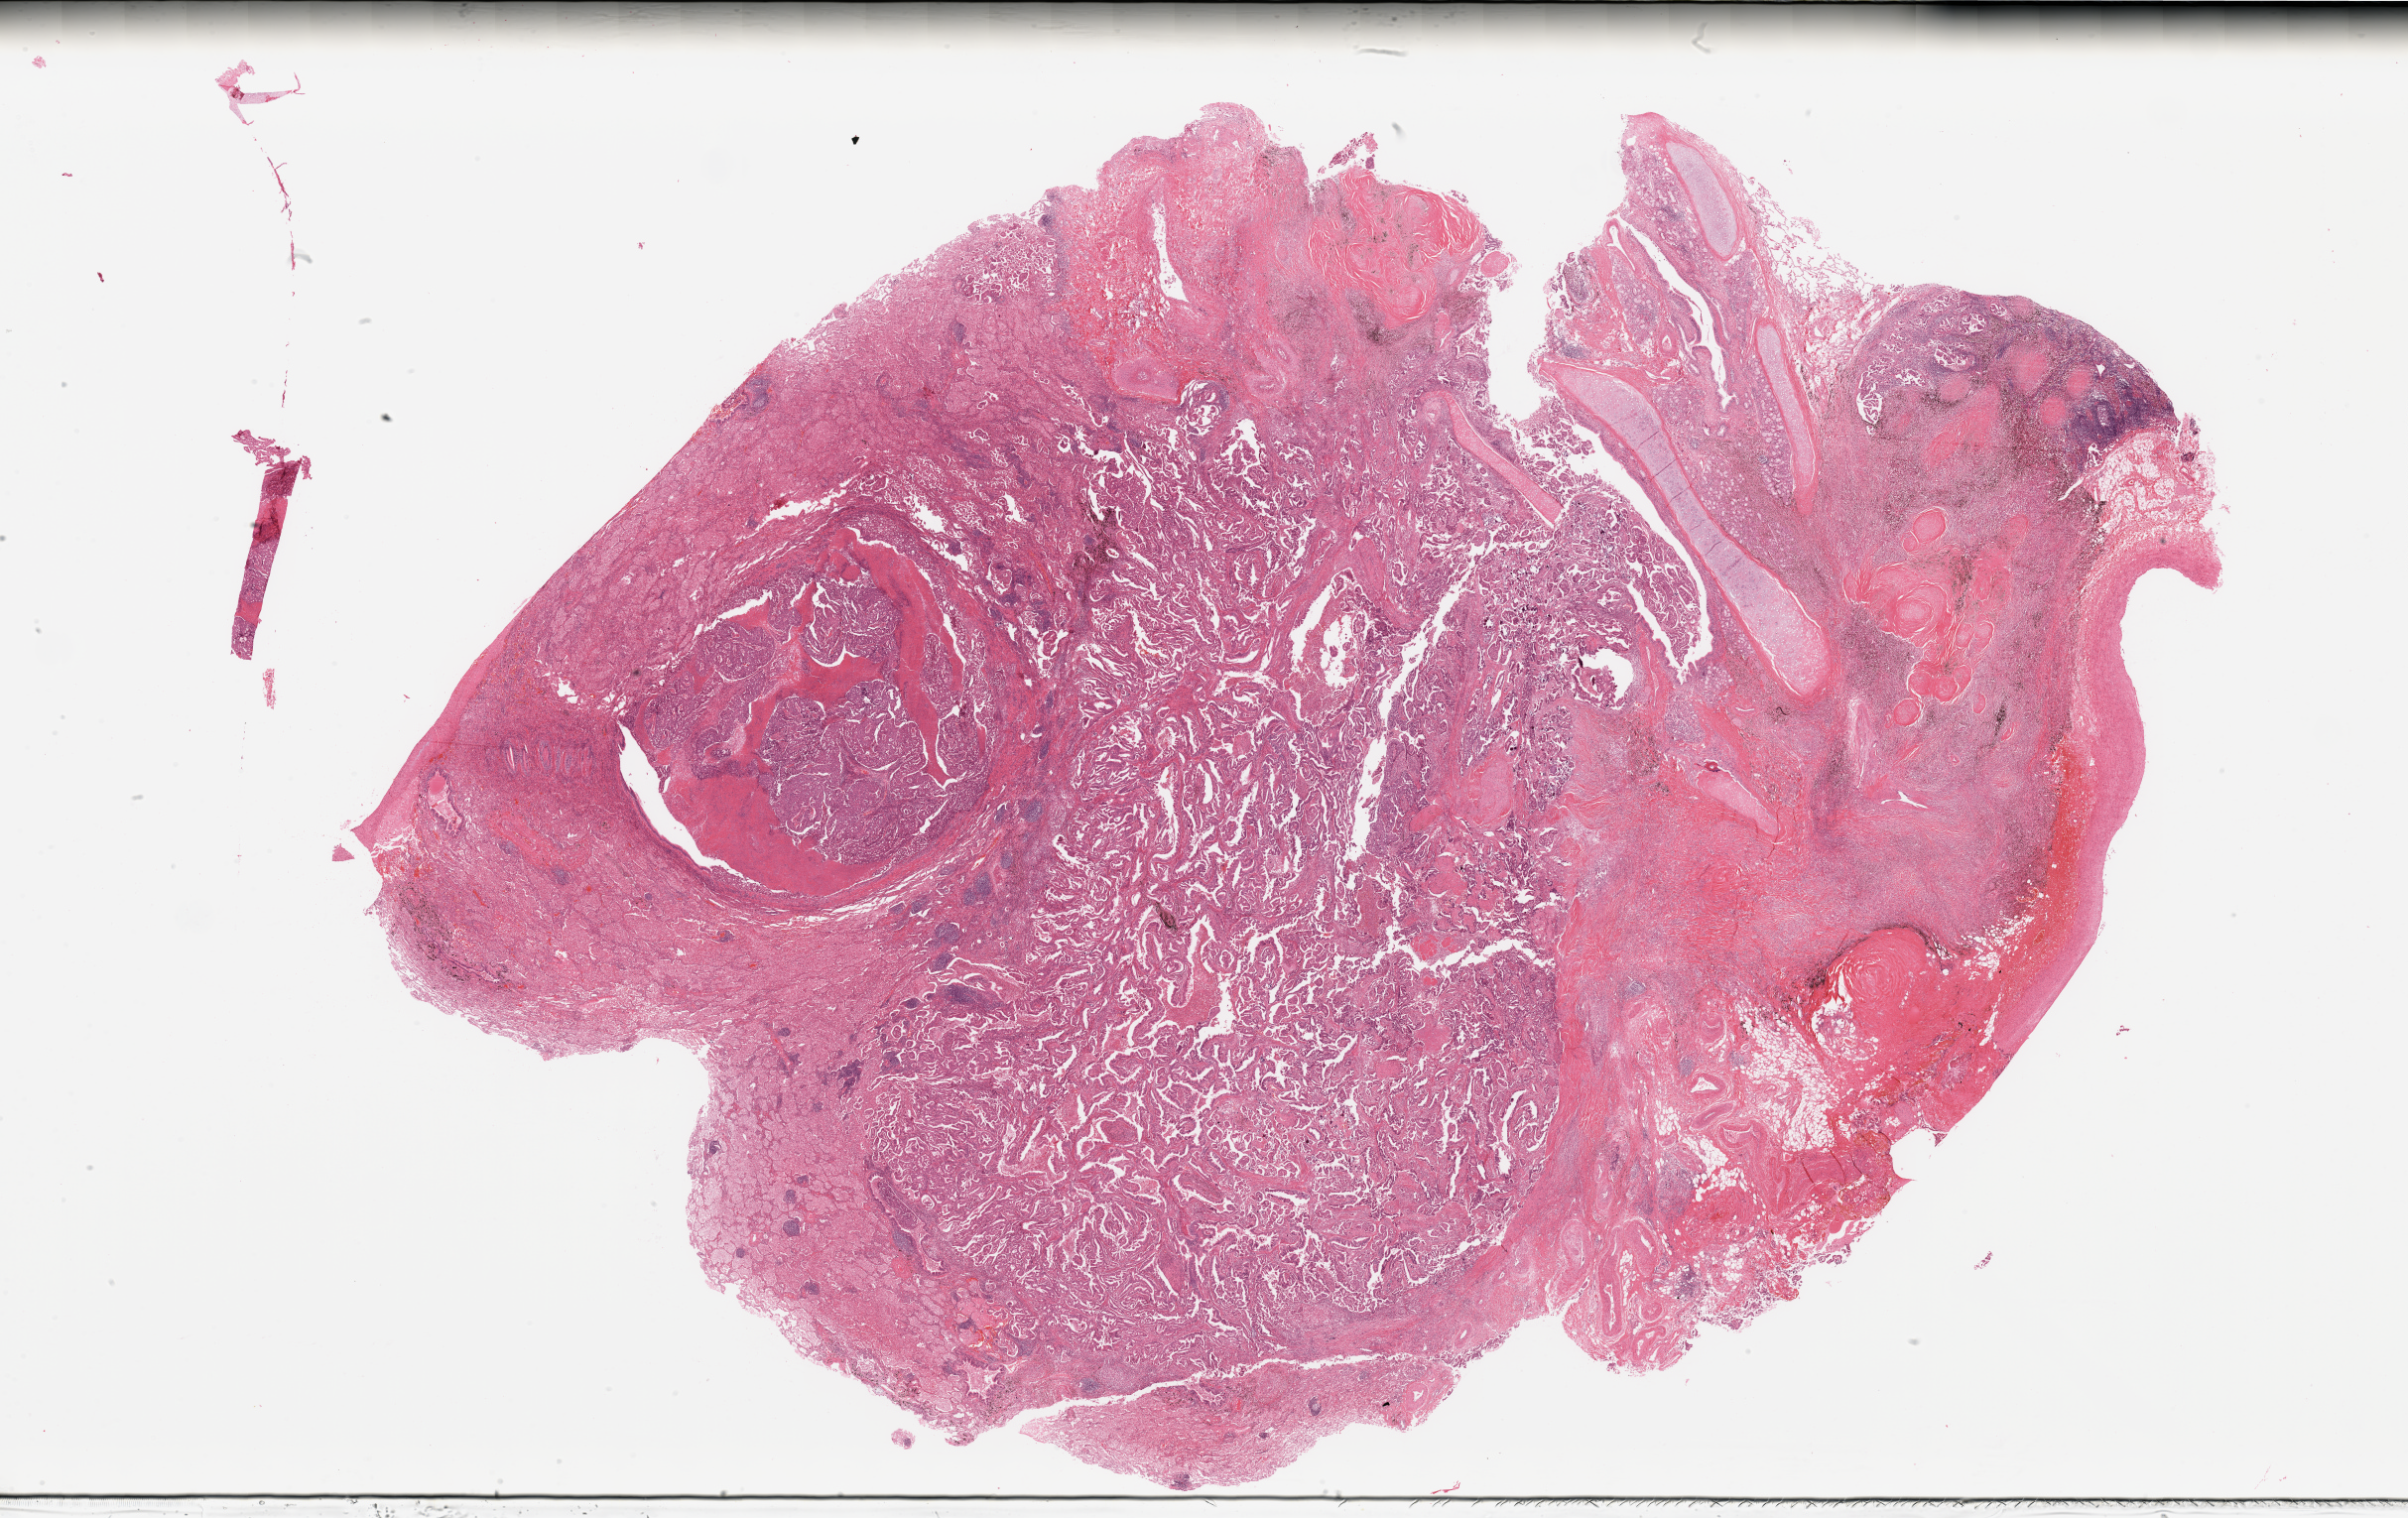
H&E-stained whole-slide image, a low-resolution overview of the entire scanned area, about 38.4 x 24.2 mm (acquisition: 20x scan). Lung, tumour tissue. Patient: male, age 67 years. Histologic grade: G2 (moderately differentiated).
Diagnosis: Adenocarcinoma, NOS. AJCC pathologic stage: IIIA.